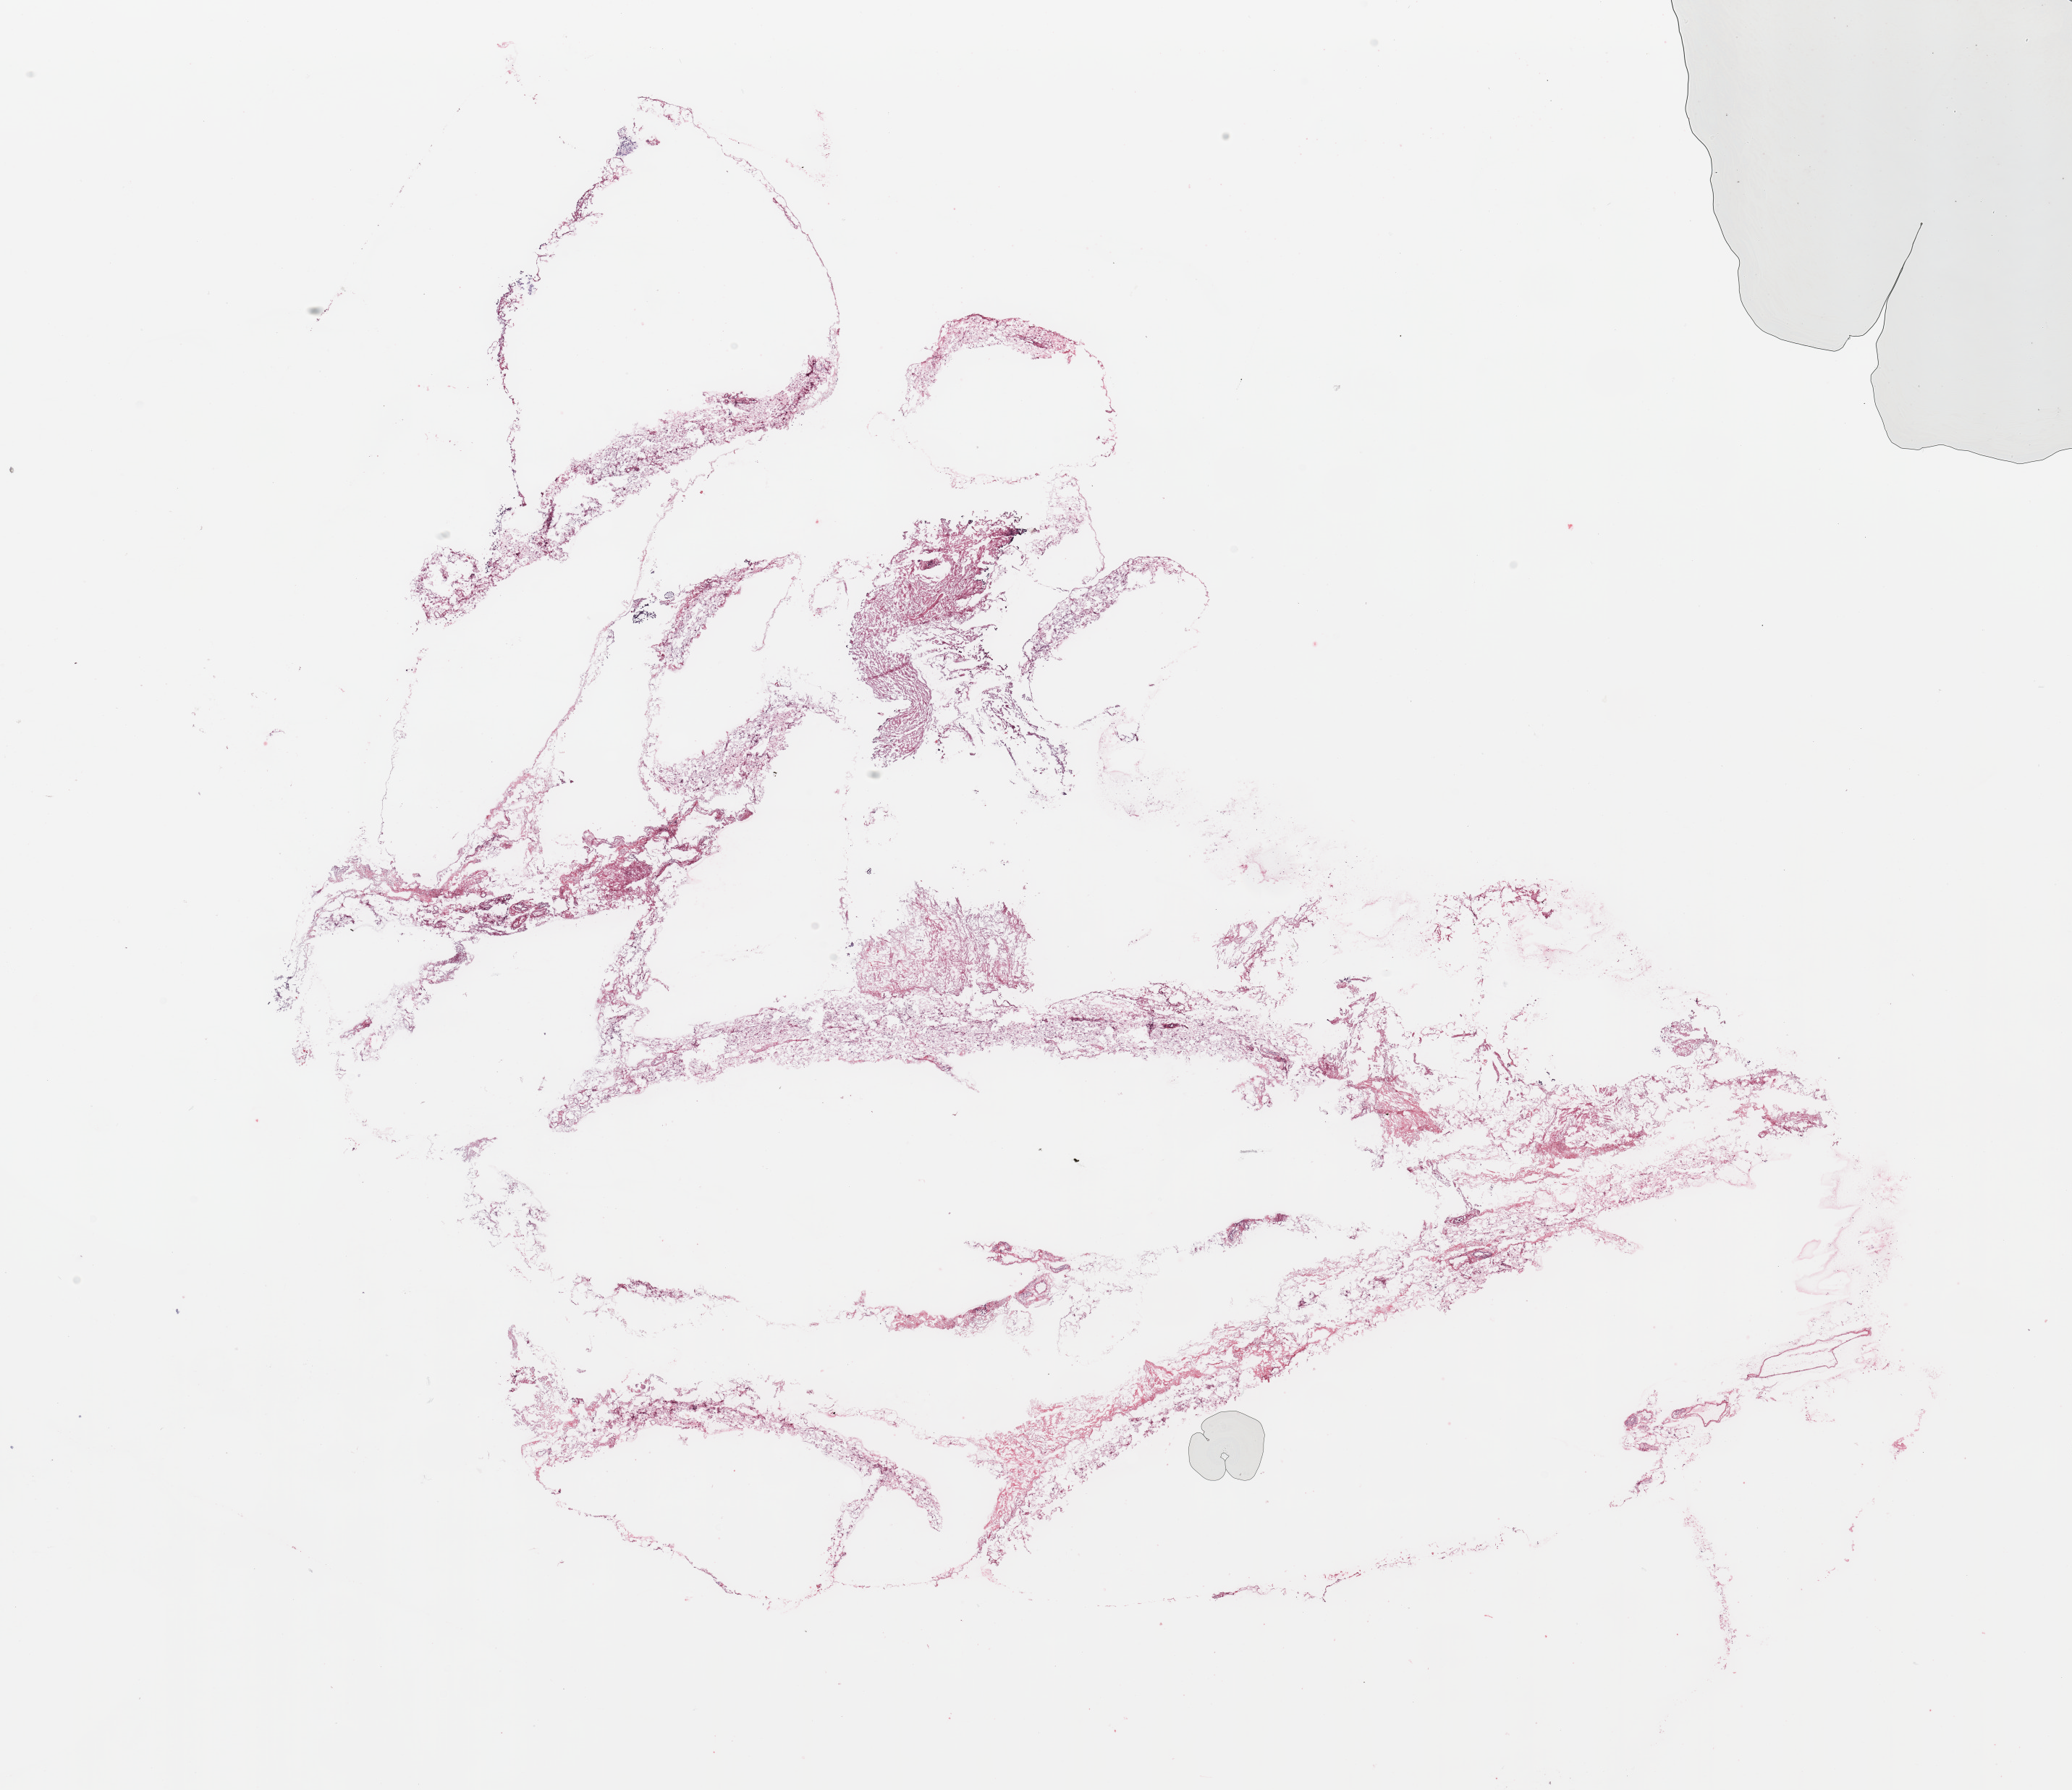
Digitized Hematoxylin and eosin (H&E) stained tissue section (whole slide), a low-resolution overview of the entire scanned area, about 22.6 x 19.6 mm (from a 20x scan); breast, tumour tissue. Female, 80 y/o.
- AJCC pathologic stage: IIA
- histologic diagnosis: Infiltrating duct carcinoma, NOS